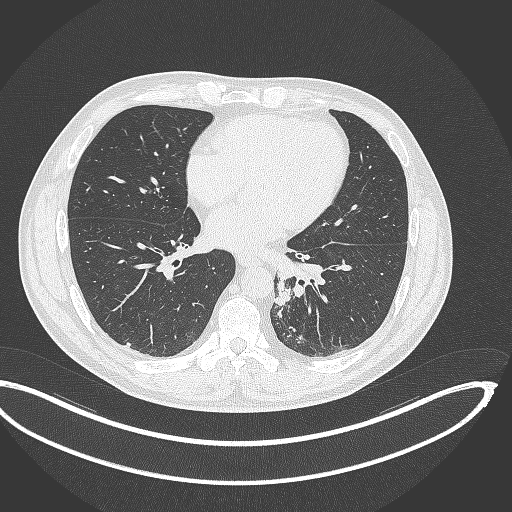
Chest CT, one axial slice. Position 144 of 362 along the scan axis. Reconstruction kernel B70f. Lung window (W 1500 / L -600 HU). 1 mm slice thickness. 512 × 512 image matrix, field of view 442 × 442 mm. Patient: male, 50 years. From the clinical record (not read from this slice): clinical TNM (as recorded): T2a N3 M0.
Outlined on this slice (rectangle marked by the reading radiologist):
- lung tumour (recorded histology: squamous cell carcinoma): box from (x=272, y=276) to (x=295, y=309) px